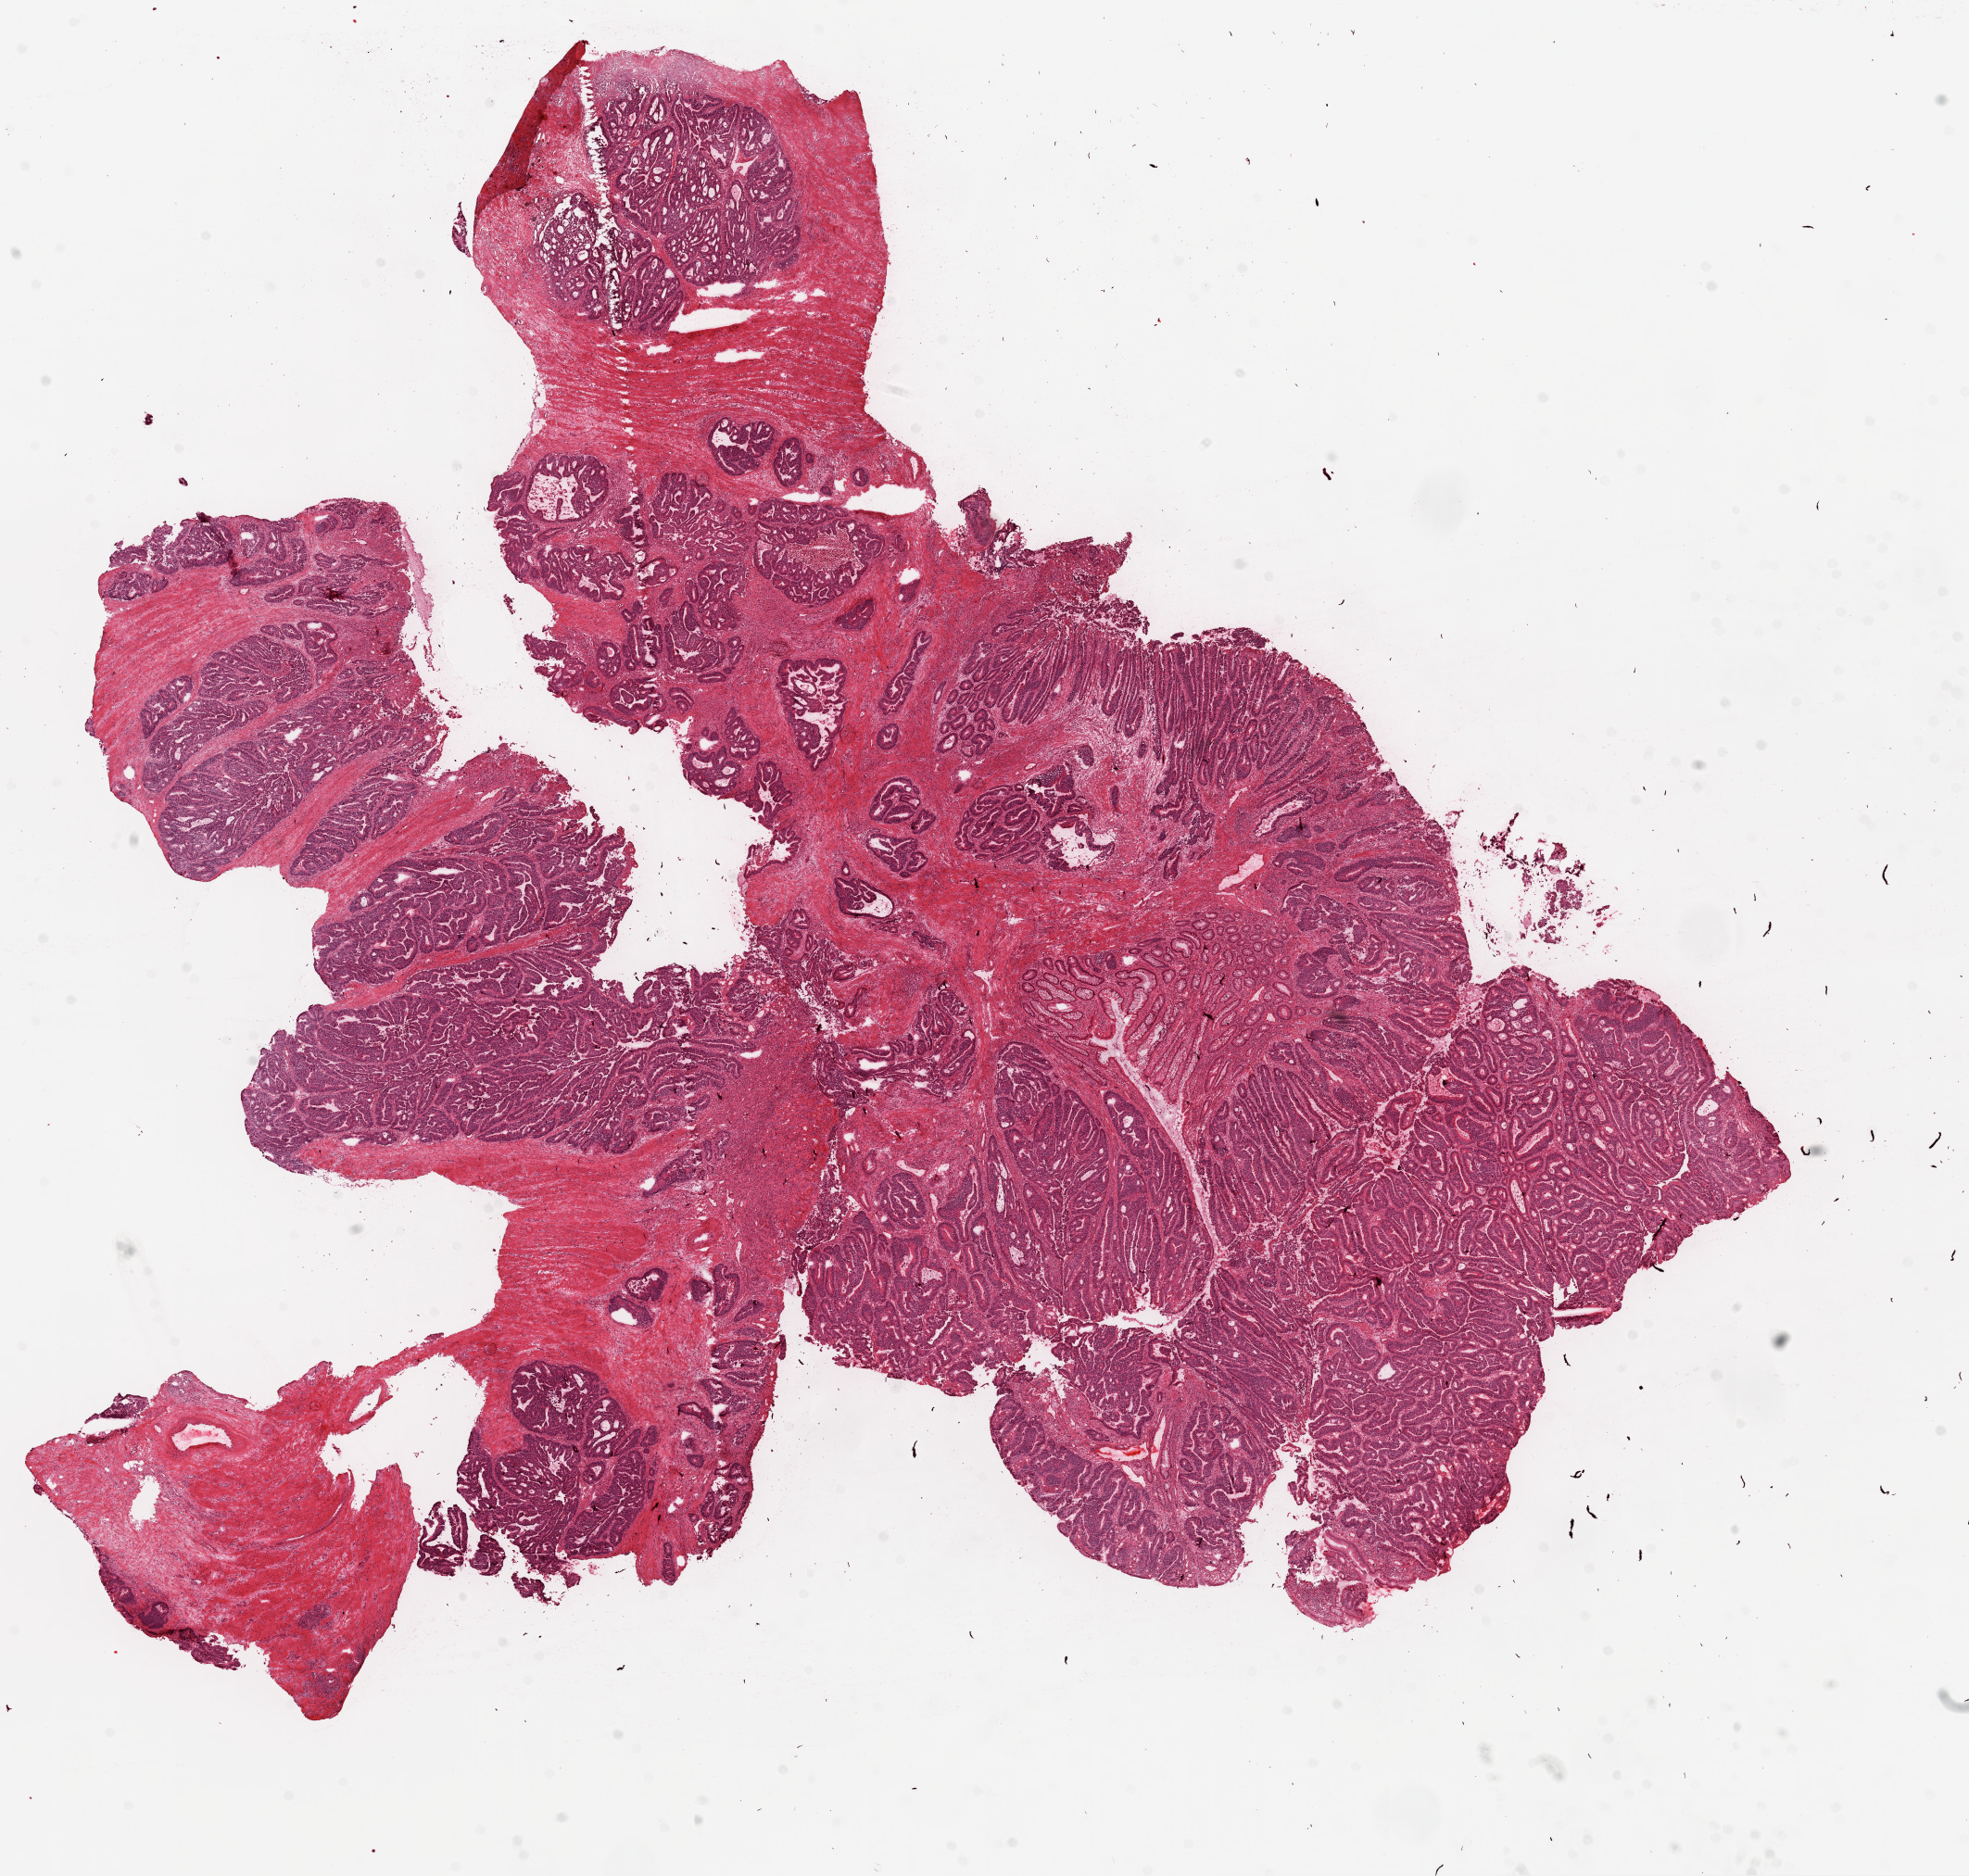
Whole-slide histology image, H&E, whole scanned area (about 17.1 x 16.2 mm, acquisition: 20x scan) shown as a low-resolution overview; frozen section; sample: primary tumour, rectum. Female patient; age at initial diagnosis 49 years. Pathologist review of this section (percent, as recorded): tumour cells 77%, tumour nuclei 75%, normal cells 0%, stromal cells 20%, necrosis 3%.
* AJCC pathologic stage: IIIB (7th edition)
* pathologic diagnosis: Adenocarcinoma, NOS
* lymph nodes positive (case pathology): 1 of 22 examined